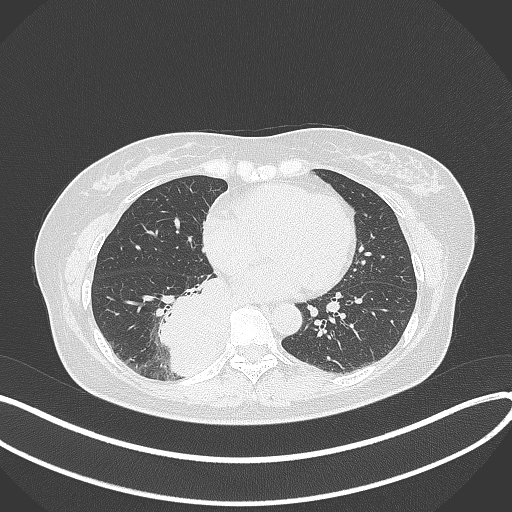
Chest CT, one axial slice. Reconstruction kernel B70f. 120 kVp. Lung window (W 1500 / L -600 HU). 1 mm slice thickness. 512 × 512 image matrix, field of view 400 × 400 mm. Female patient, age 54 years. Case-level facts recorded for this patient, not image findings: clinical TNM (as recorded): T4 N0 M0.
Structures marked on this image (bounding box drawn by a radiologist):
- lung tumour (recorded histology: adenocarcinoma): box from (x=158, y=275) to (x=233, y=386) px